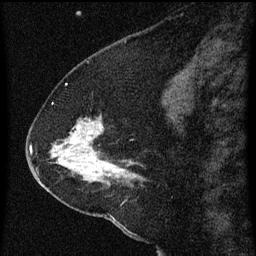
Breast MRI (dynamic contrast-enhanced), one sagittal slice; position 23 of 60 along the scan axis; dynamic contrast-enhanced series, image 2 of 3 at this slice position (ordered by acquisition); 1.5 T; TE 4.2 ms, TR 8 ms; 2 mm slice thickness; 256 × 256 image matrix, field of view 180 × 180 mm. Female patient, age 47 years.
Structures marked on this image (semi-automatic segmentation, software-assisted and operator-edited):
- analysis volume of interest (the breast-tissue region the enhancement analysis was run in; not a lesion): box from (x=36, y=98) to (x=145, y=213) px
- tumour enhancement mask (voxels above the 70 % enhancement threshold inside the analysis volume of interest): (x=51, y=118)–(x=140, y=183)